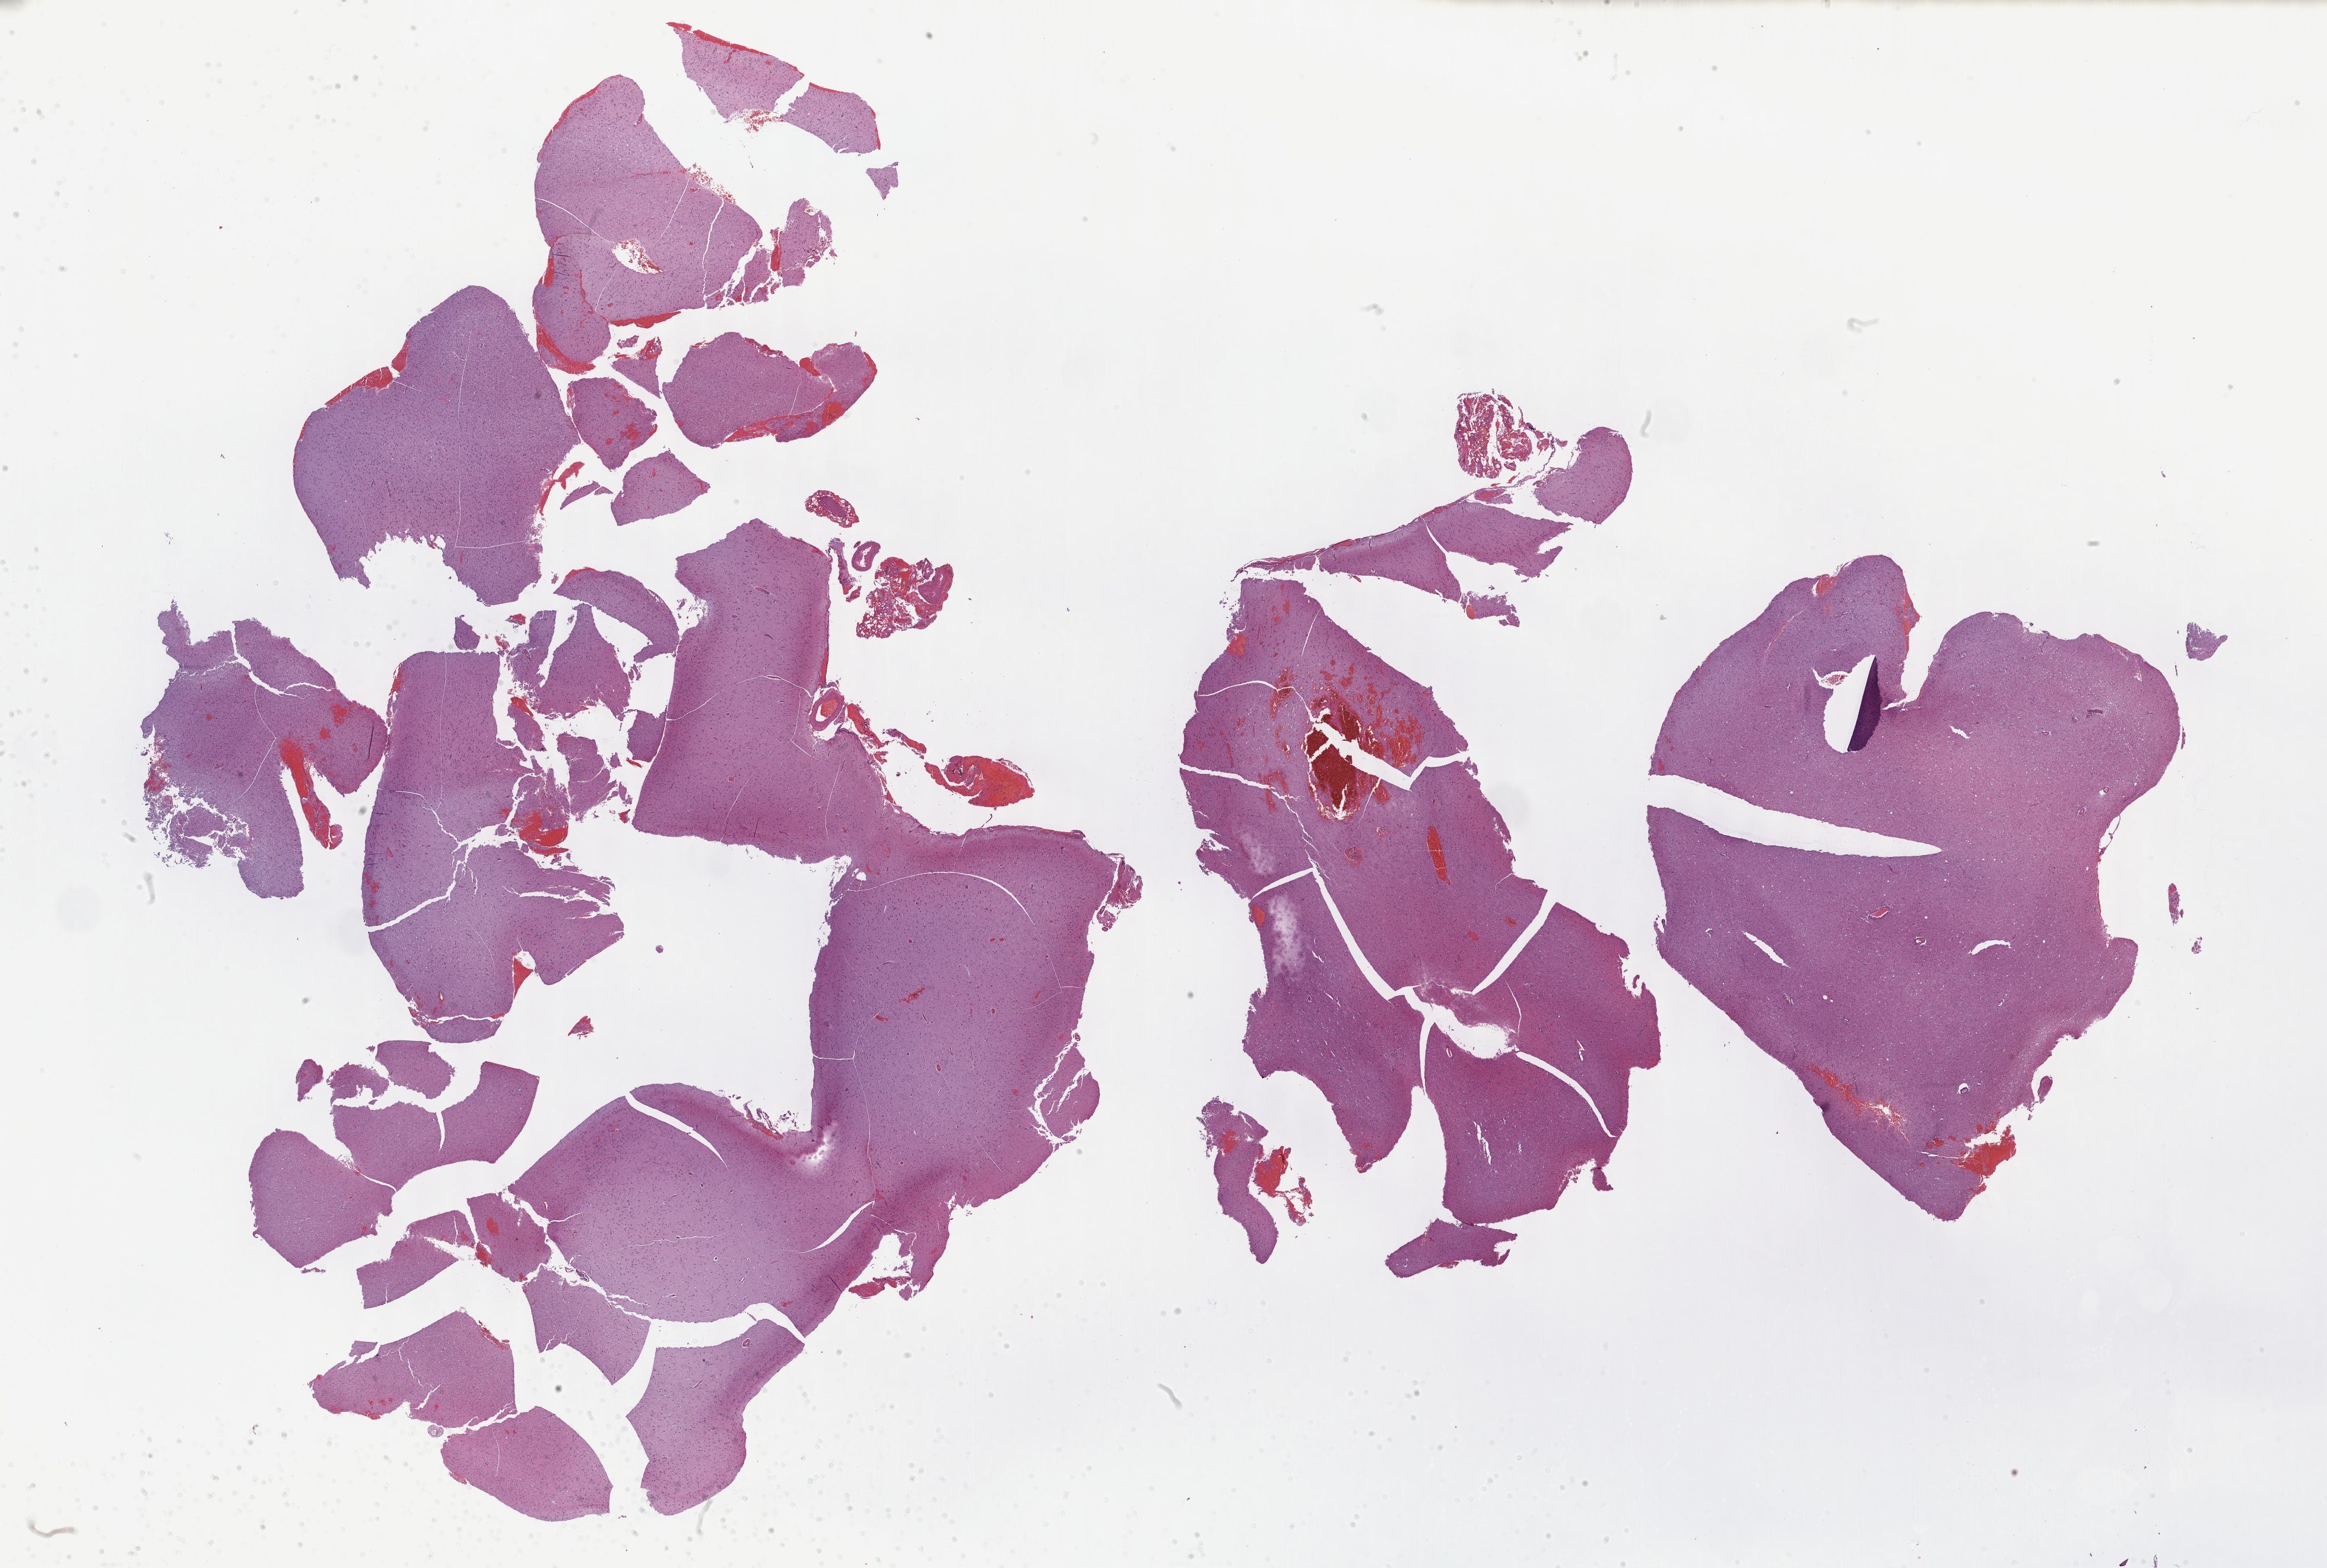
Whole-slide histology image, Hematoxylin and eosin (H&E) stained — a low-resolution overview of the entire scanned area, about 31.7 x 21.4 mm (from a 40x scan); FFPE section; brain, primary tumour sample. Male, age 58 years at initial diagnosis. Histologic grade: G3 (poorly differentiated).
Pathologic diagnosis: Astrocytoma, anaplastic (cerebrum).